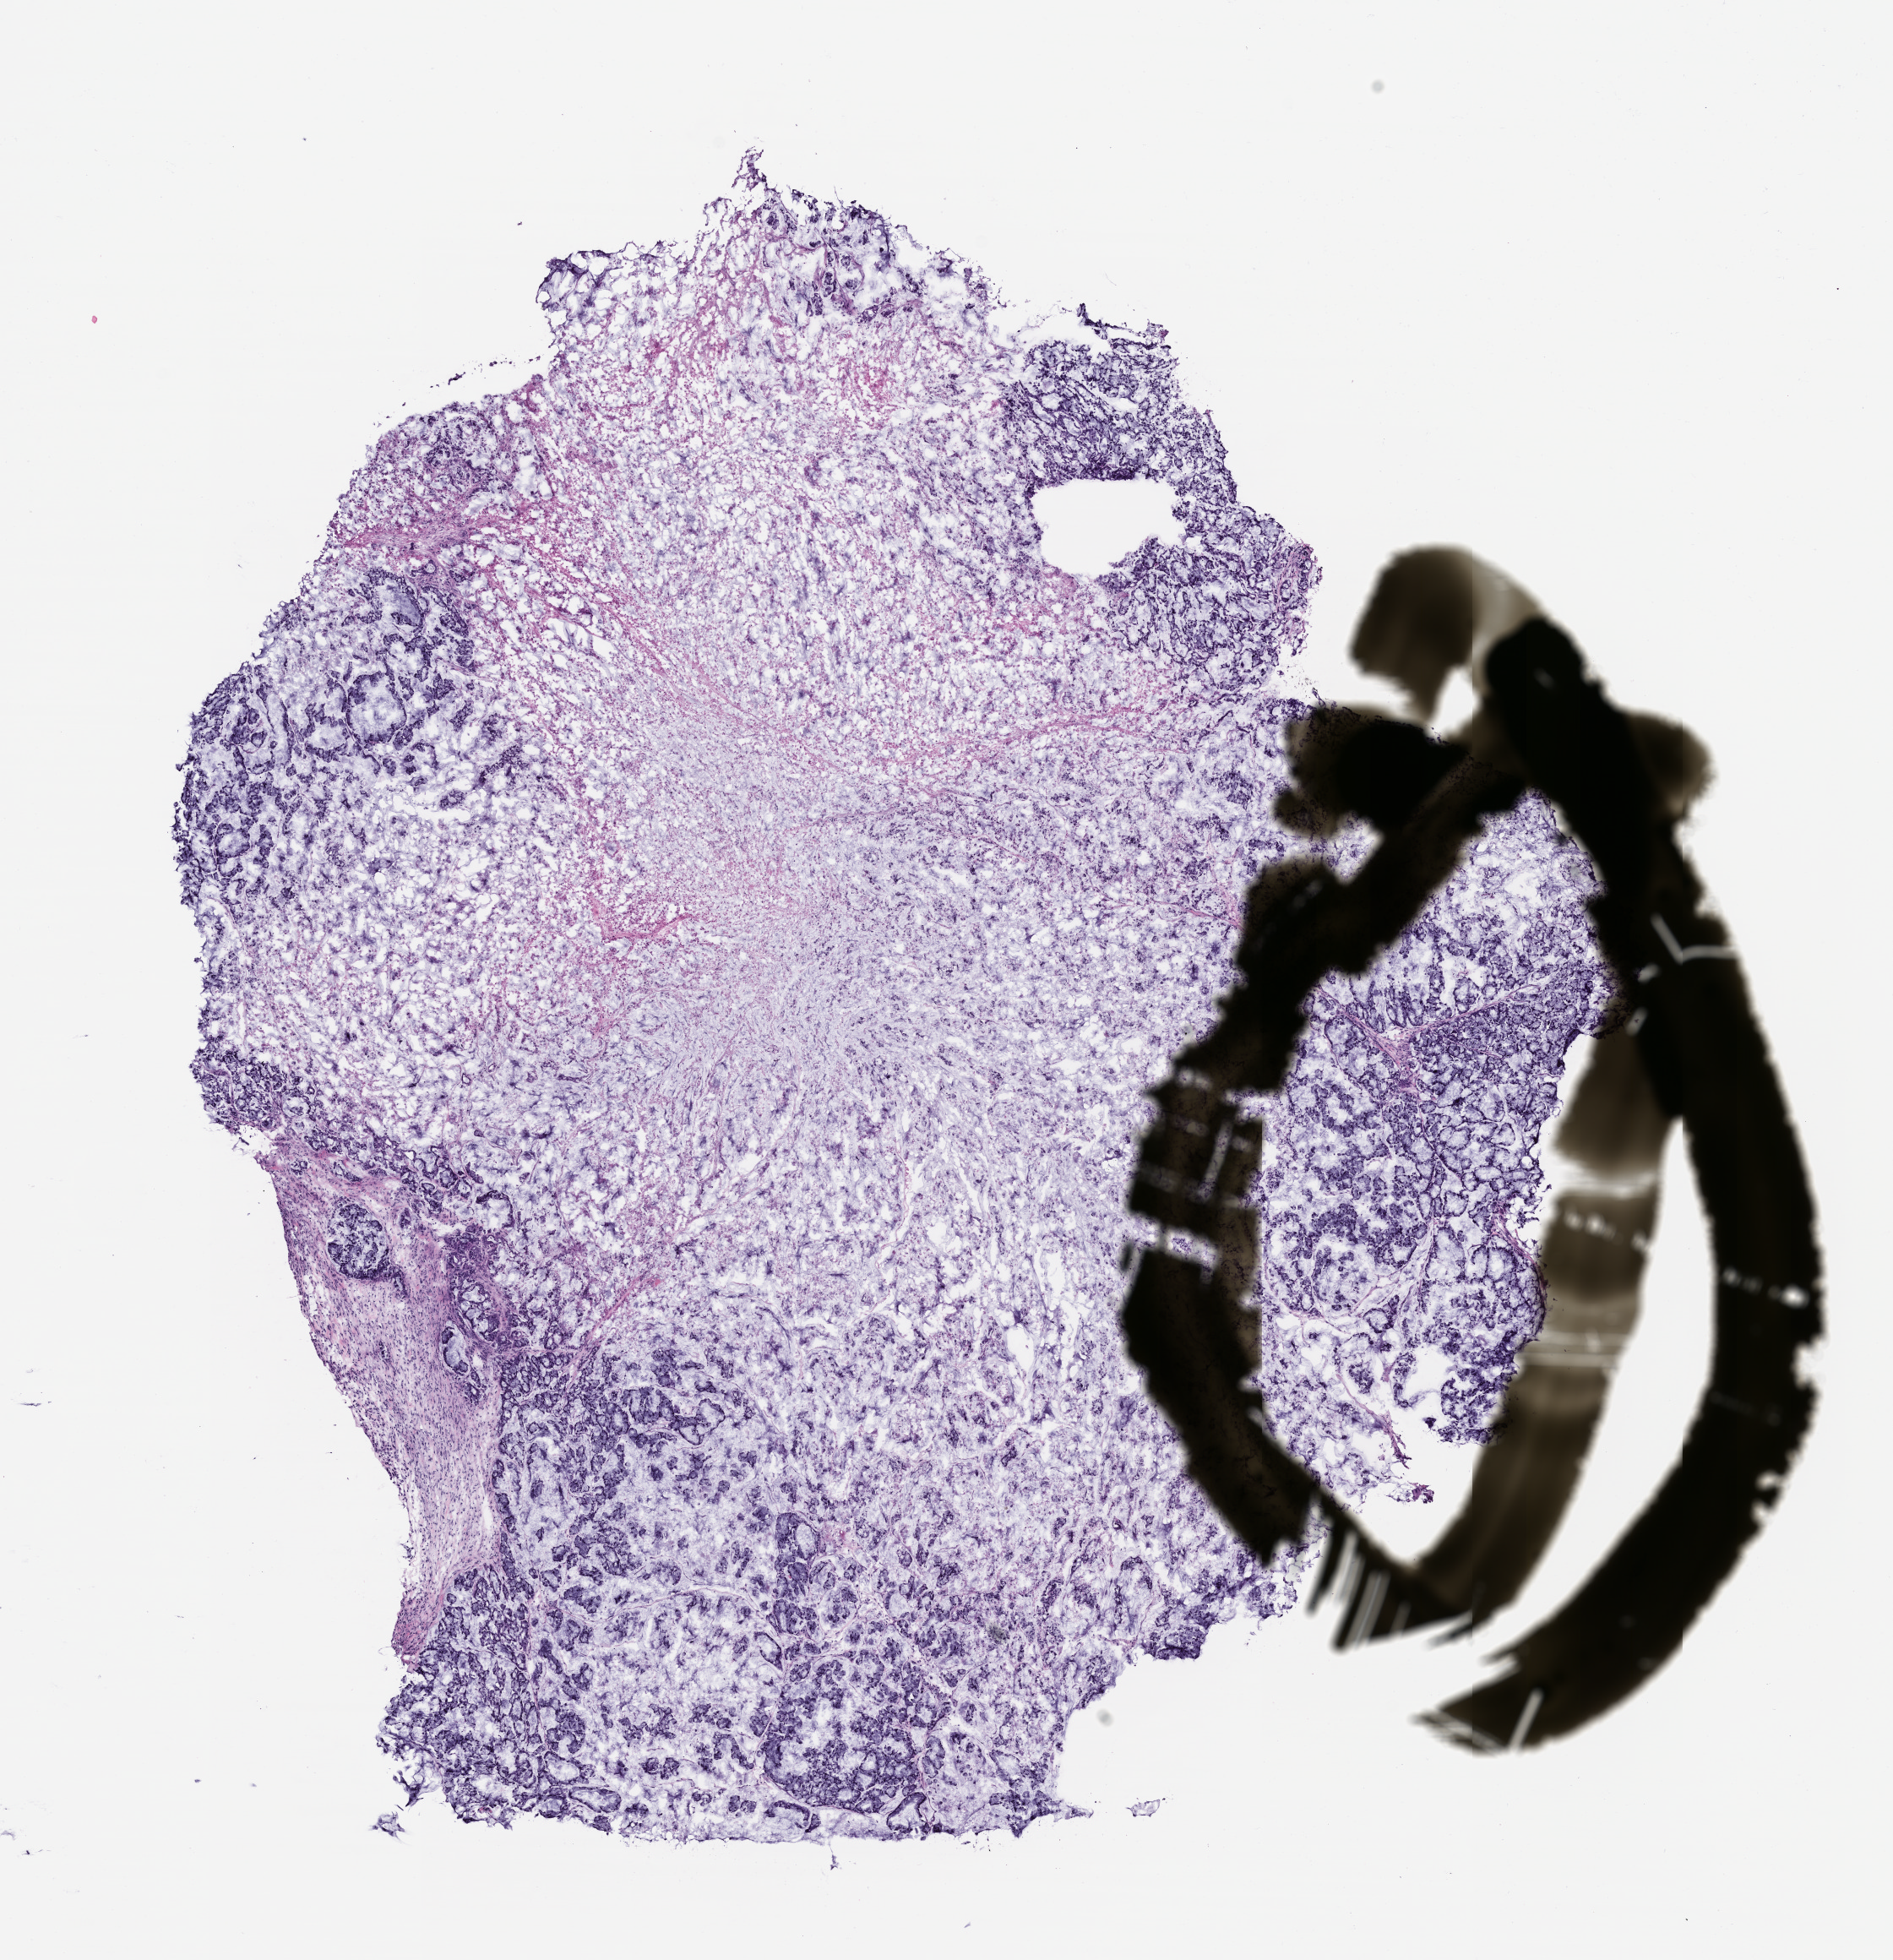
Hematoxylin and eosin (H&E) whole-slide image of a patient-derived xenograft (PDX) tumor grown in a mouse, passage 2 — shown as a low-resolution overview of the whole scanned area (about 9.0 x 9.3 mm), formalin-fixed, paraffin-embedded (FFPE) tissue, originating tumor site category: colon.
• originating patient diagnosis: Colon Adenocarcinoma